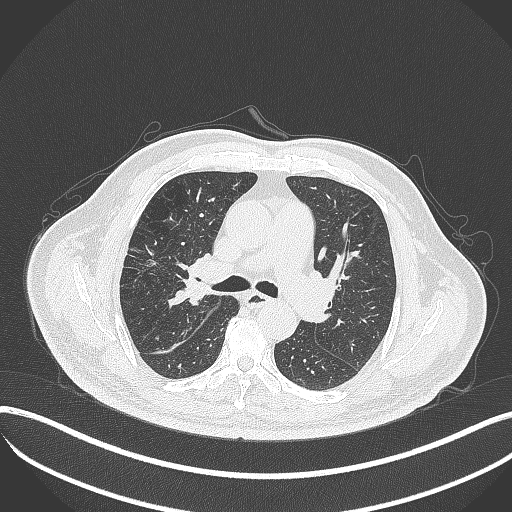
Chest CT, one axial slice. Slice 227 of 401 in the series (ordered by position). Reconstruction kernel B70f. Lung window (W 1500 / L -600 HU). 1 mm slice thickness. 512 × 512 image matrix, field of view 400 × 400 mm. Patient: male, 72 years. From the clinical record (not read from this slice): clinical TNM (as recorded): T1c N0 M0; histopathological grade: G2.
Structures marked on this image (rectangle marked by the reading radiologist):
- lung tumour (recorded histology: squamous cell carcinoma): bounding box (x1, y1, x2, y2) in pixels: (162, 253, 199, 308)